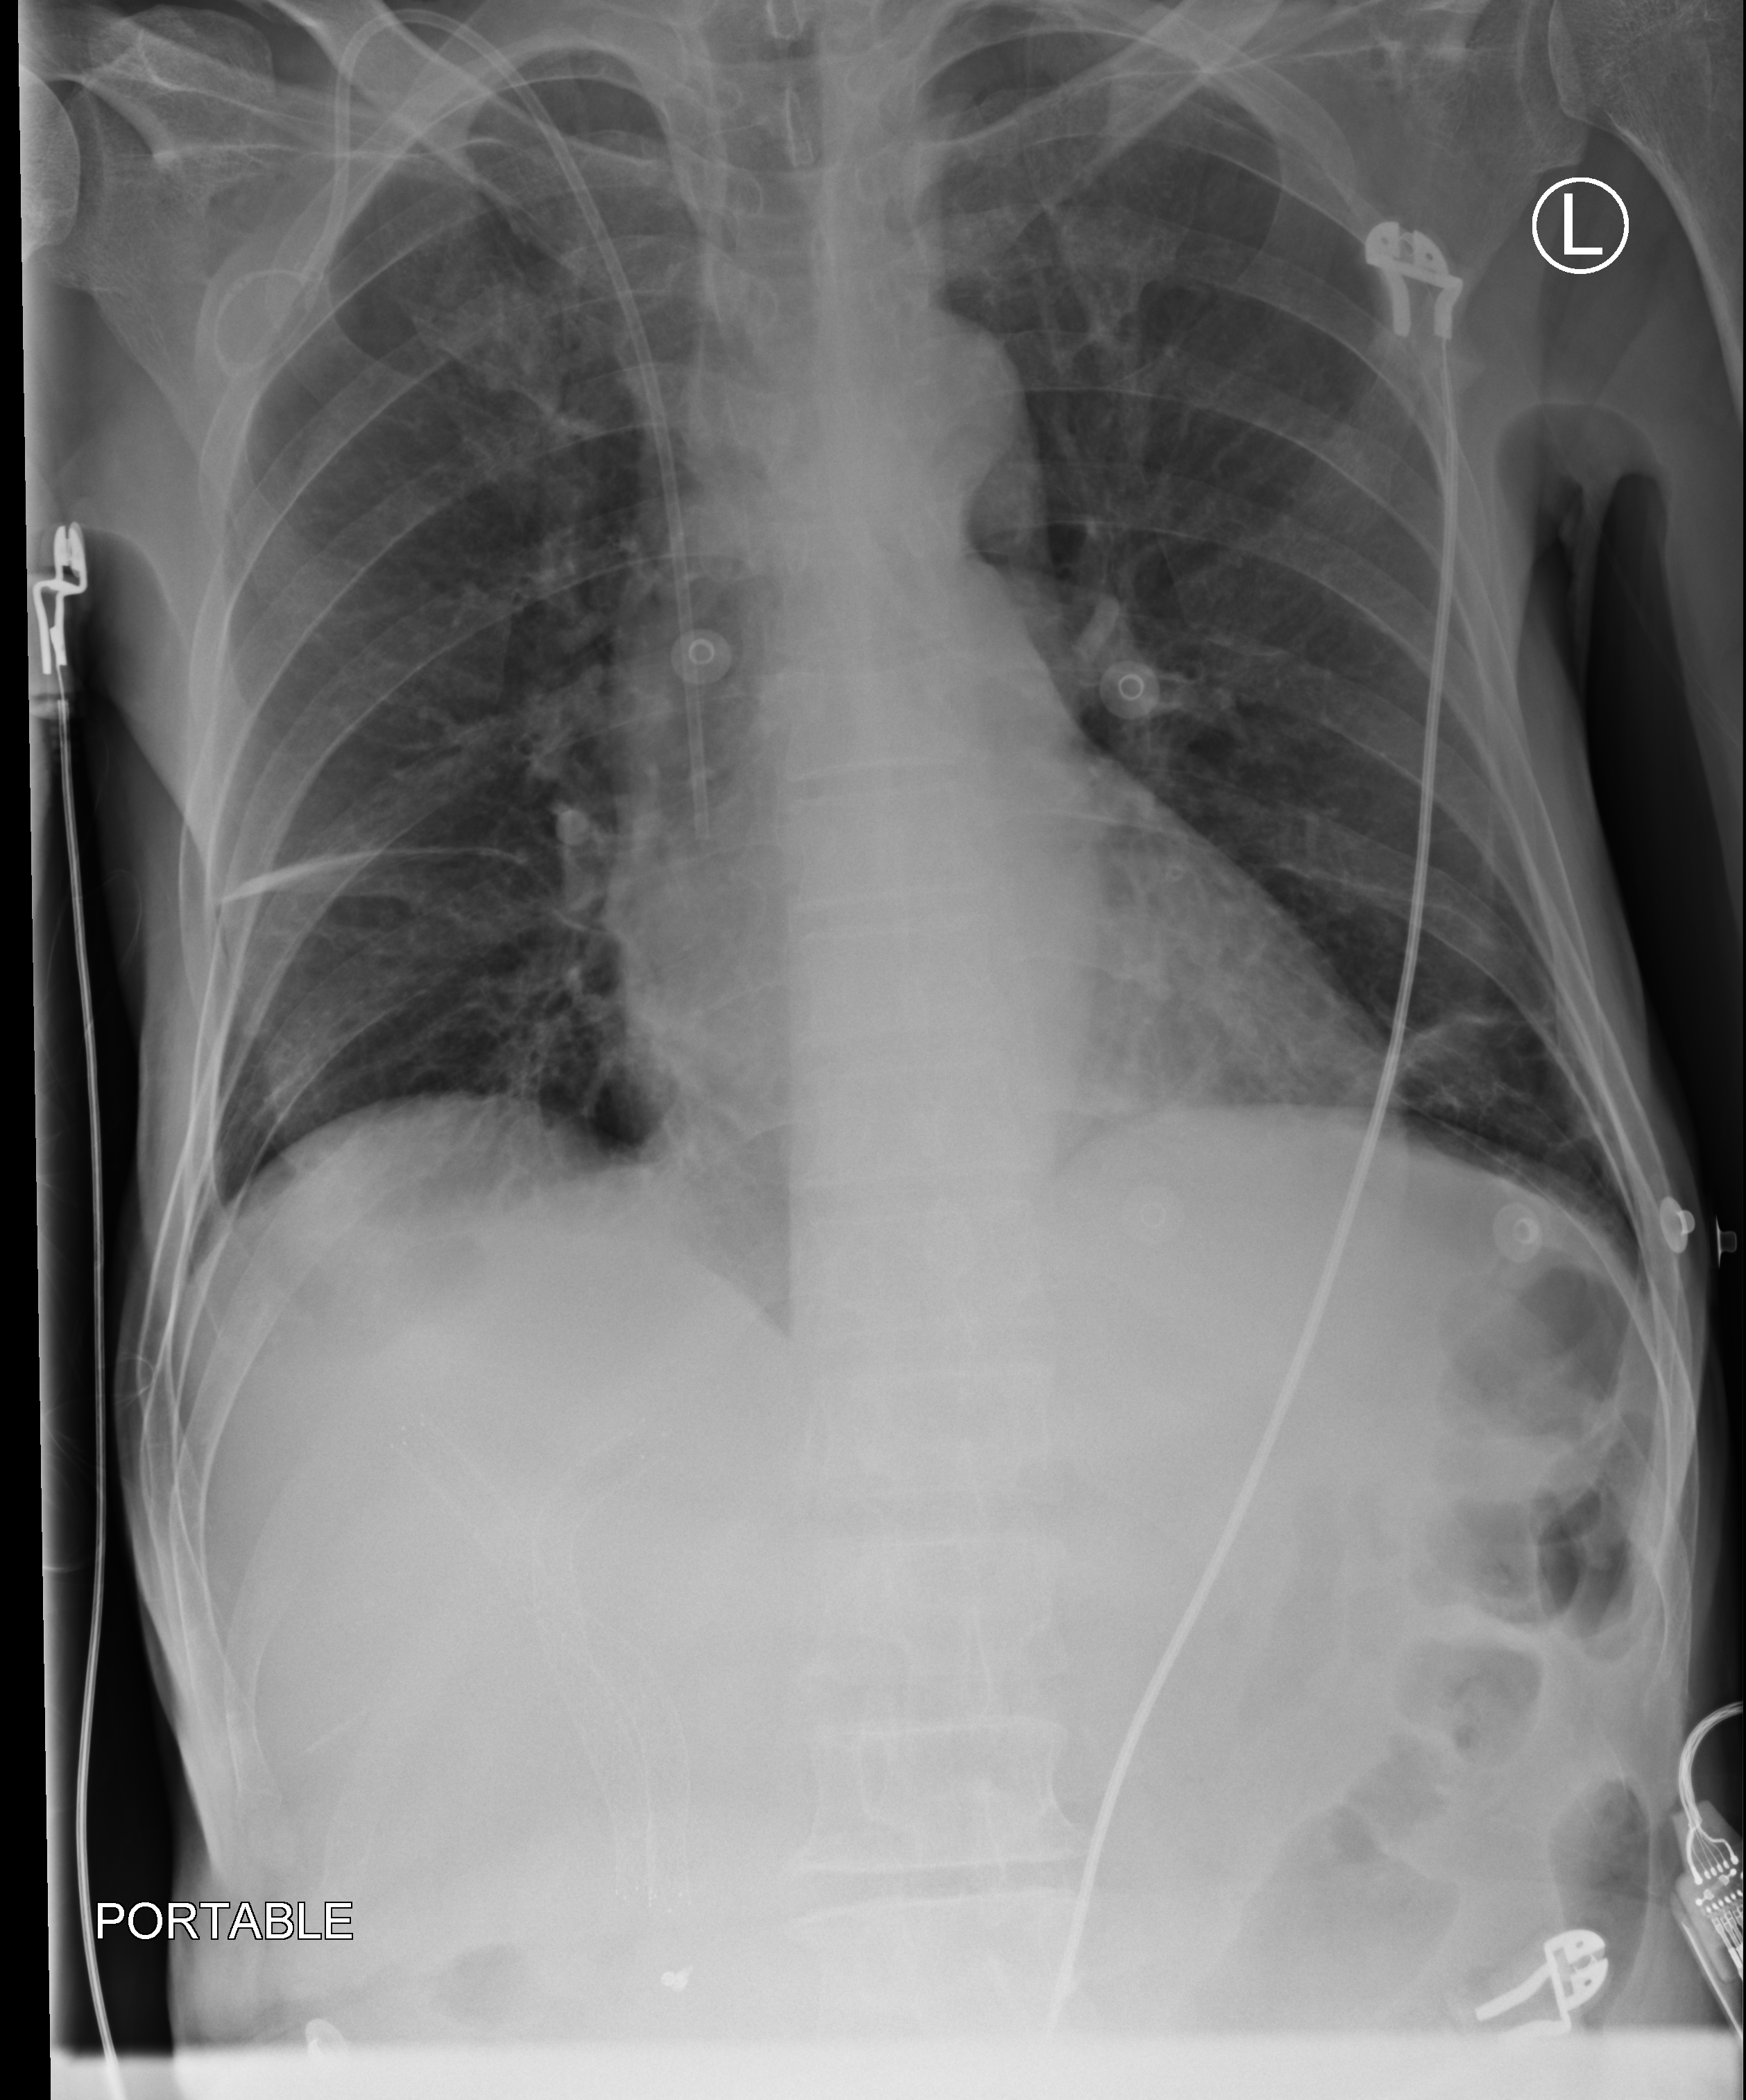
Chest X-ray (portable), anteroposterior (AP) projection. Male patient hospitalised with COVID-19, age 60–74 years.
Hospital-stay facts (about this admission, not read from this image; timing relative to this image not recorded):
- admitted to intensive care during this hospital stay: no
- mechanically ventilated during this hospital stay: no